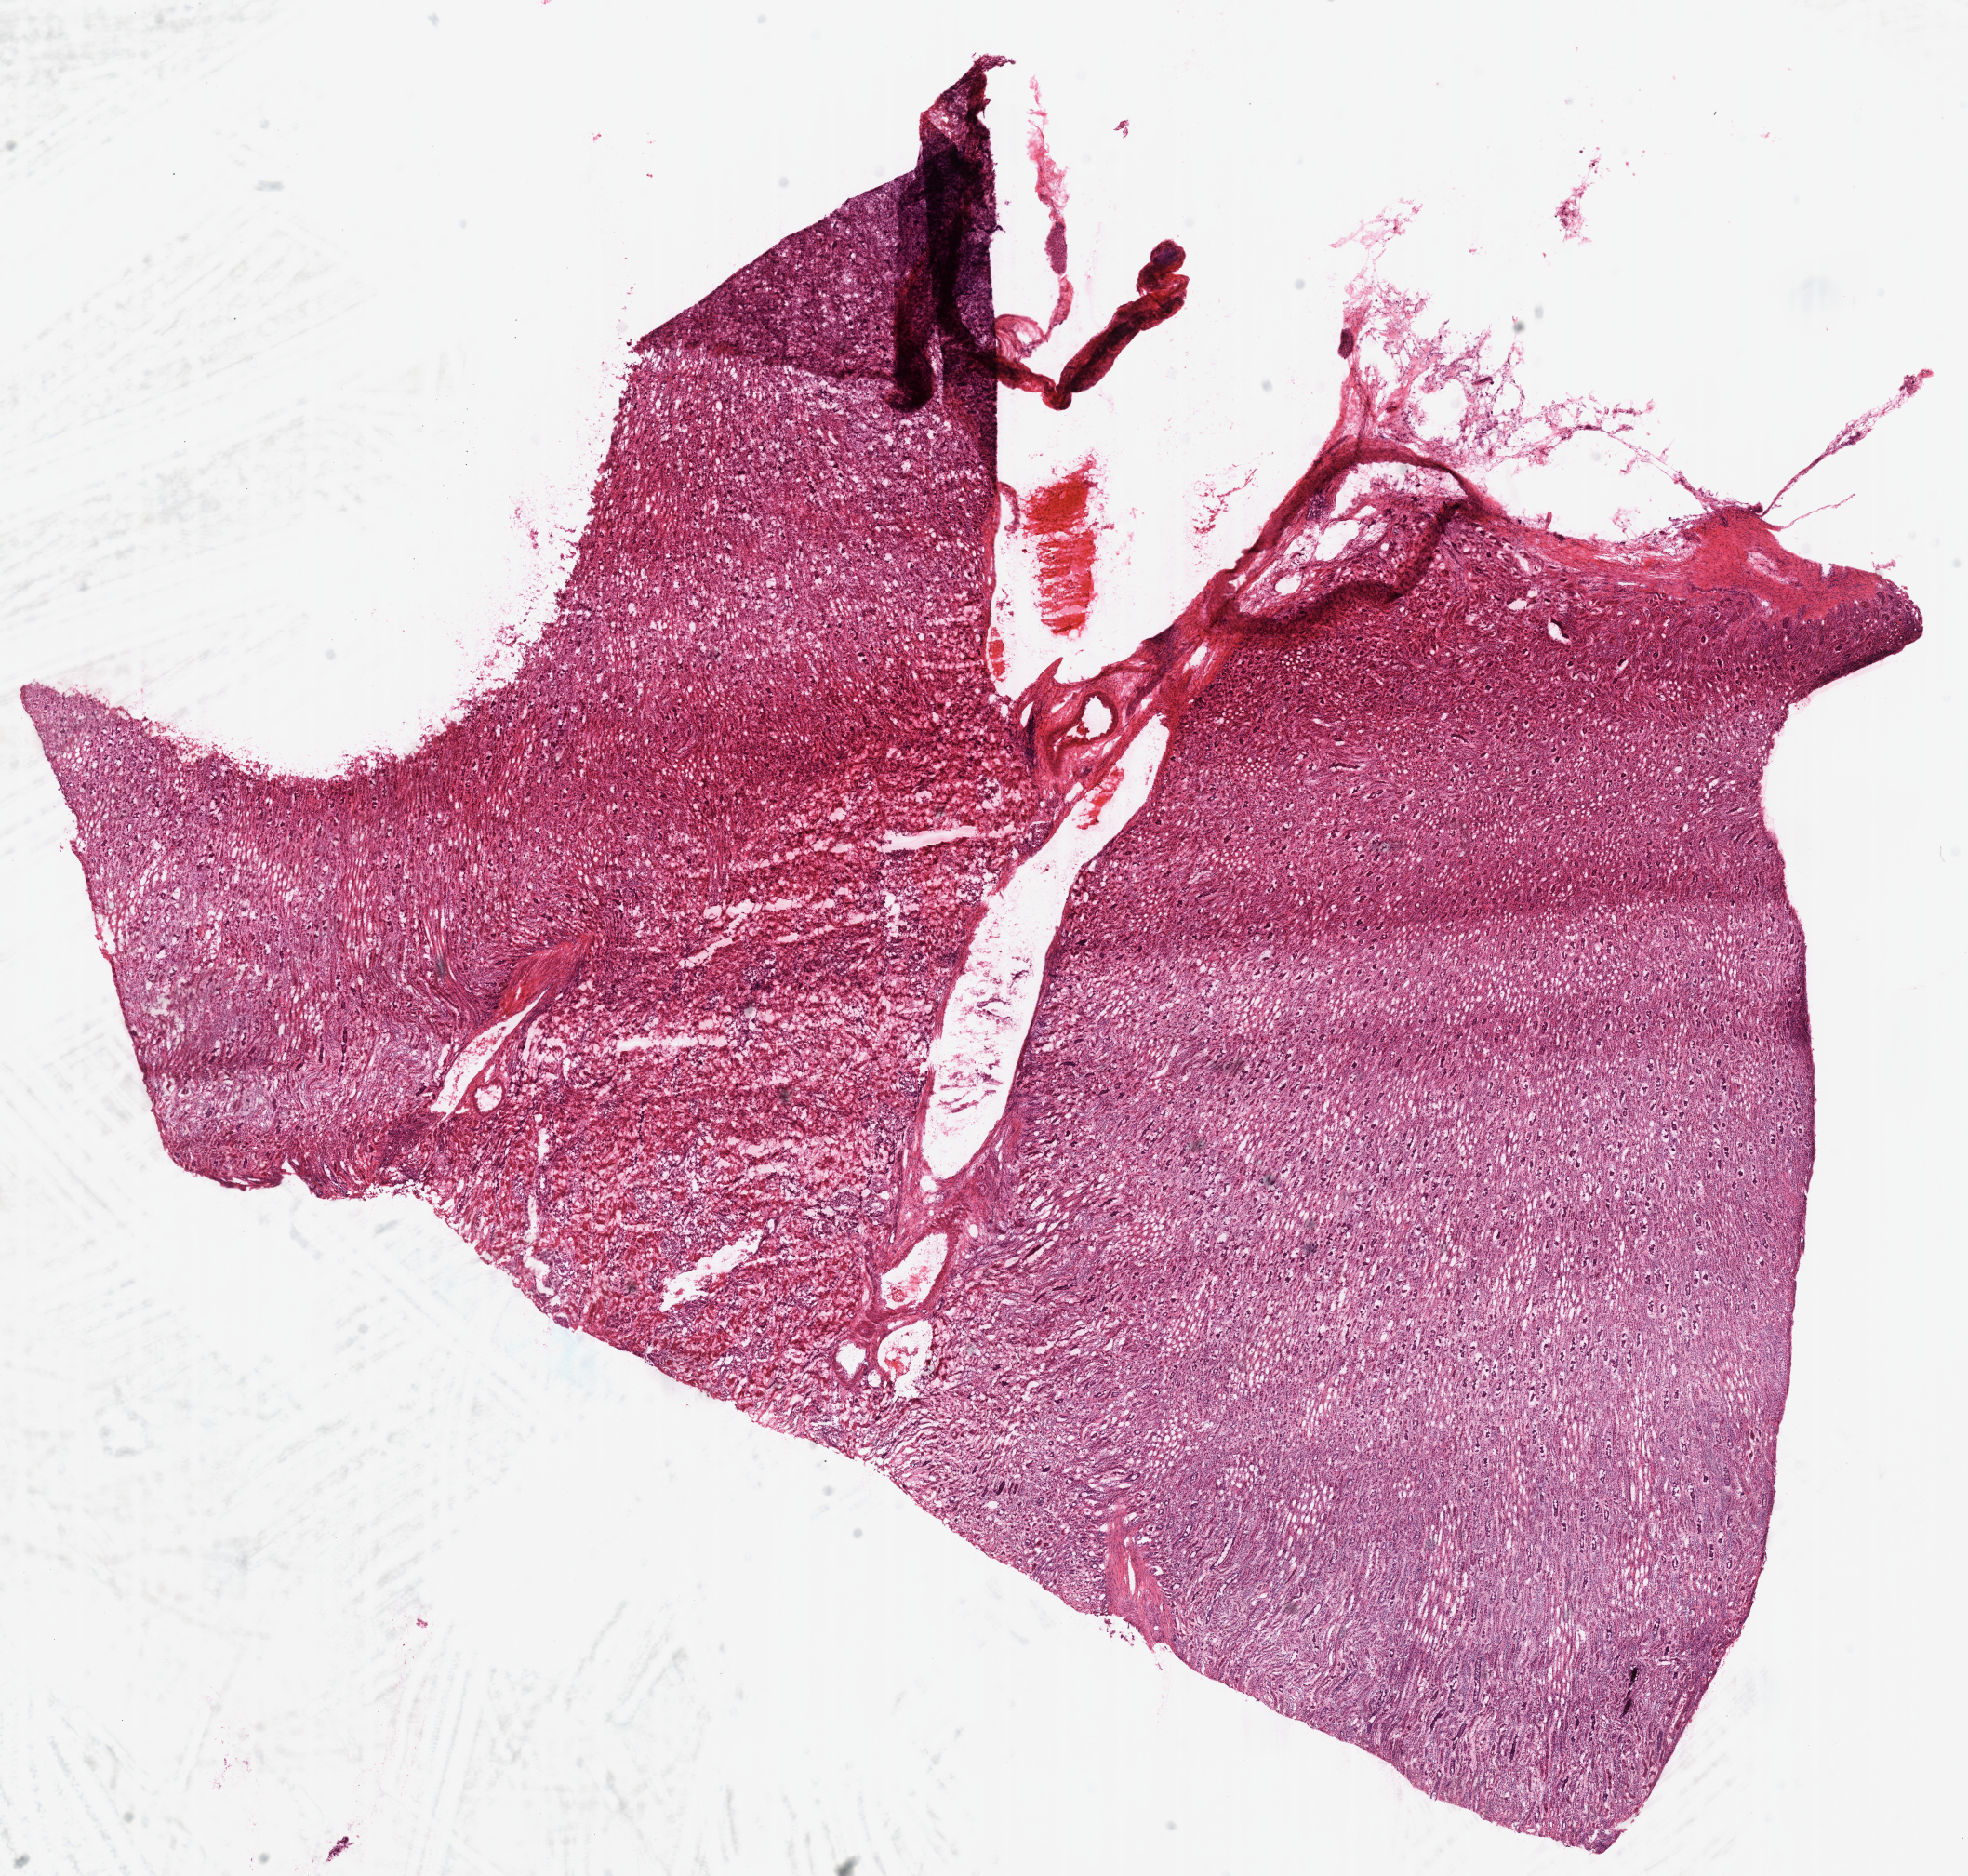
Whole-slide histology image, H&E-stained, low-resolution overview of the scanned area, about 16.6 x 15.9 mm; frozen section; solid tissue normal (non-tumour tissue) sample from the kidney. Patient: female, age at initial diagnosis 28 years. Inflammatory infiltration, as recorded: lymphocyte infiltration 0%, monocyte infiltration 0%, neutrophil infiltration 0%.
This section: solid tissue normal (non-tumour) sample from the same patient. Patient diagnosis: Renal cell carcinoma, chromophobe type.